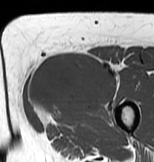
MRI of an extremity soft-tissue mass, one axial slice. Position 30 of 83 along the scan axis. MR volume resampled by the dataset authors to the PET/CT grid (not the native acquisition matrix). 3.27 mm slice thickness. 154 × 162 image matrix. Female patient. Case-level facts recorded for this patient, not image findings: histological type: myxofibrosarcoma; grade: intermediate; site of the primary tumour: left thigh.
Structures marked on this image (expert contour drawn on MRI and transferred to this co-registered scan by the dataset authors):
- gross tumour volume including surrounding oedema: bounding box <26,54,120,126> (left, top, right, bottom; pixels)
- gross tumour volume (mass): <28,52,116,115>